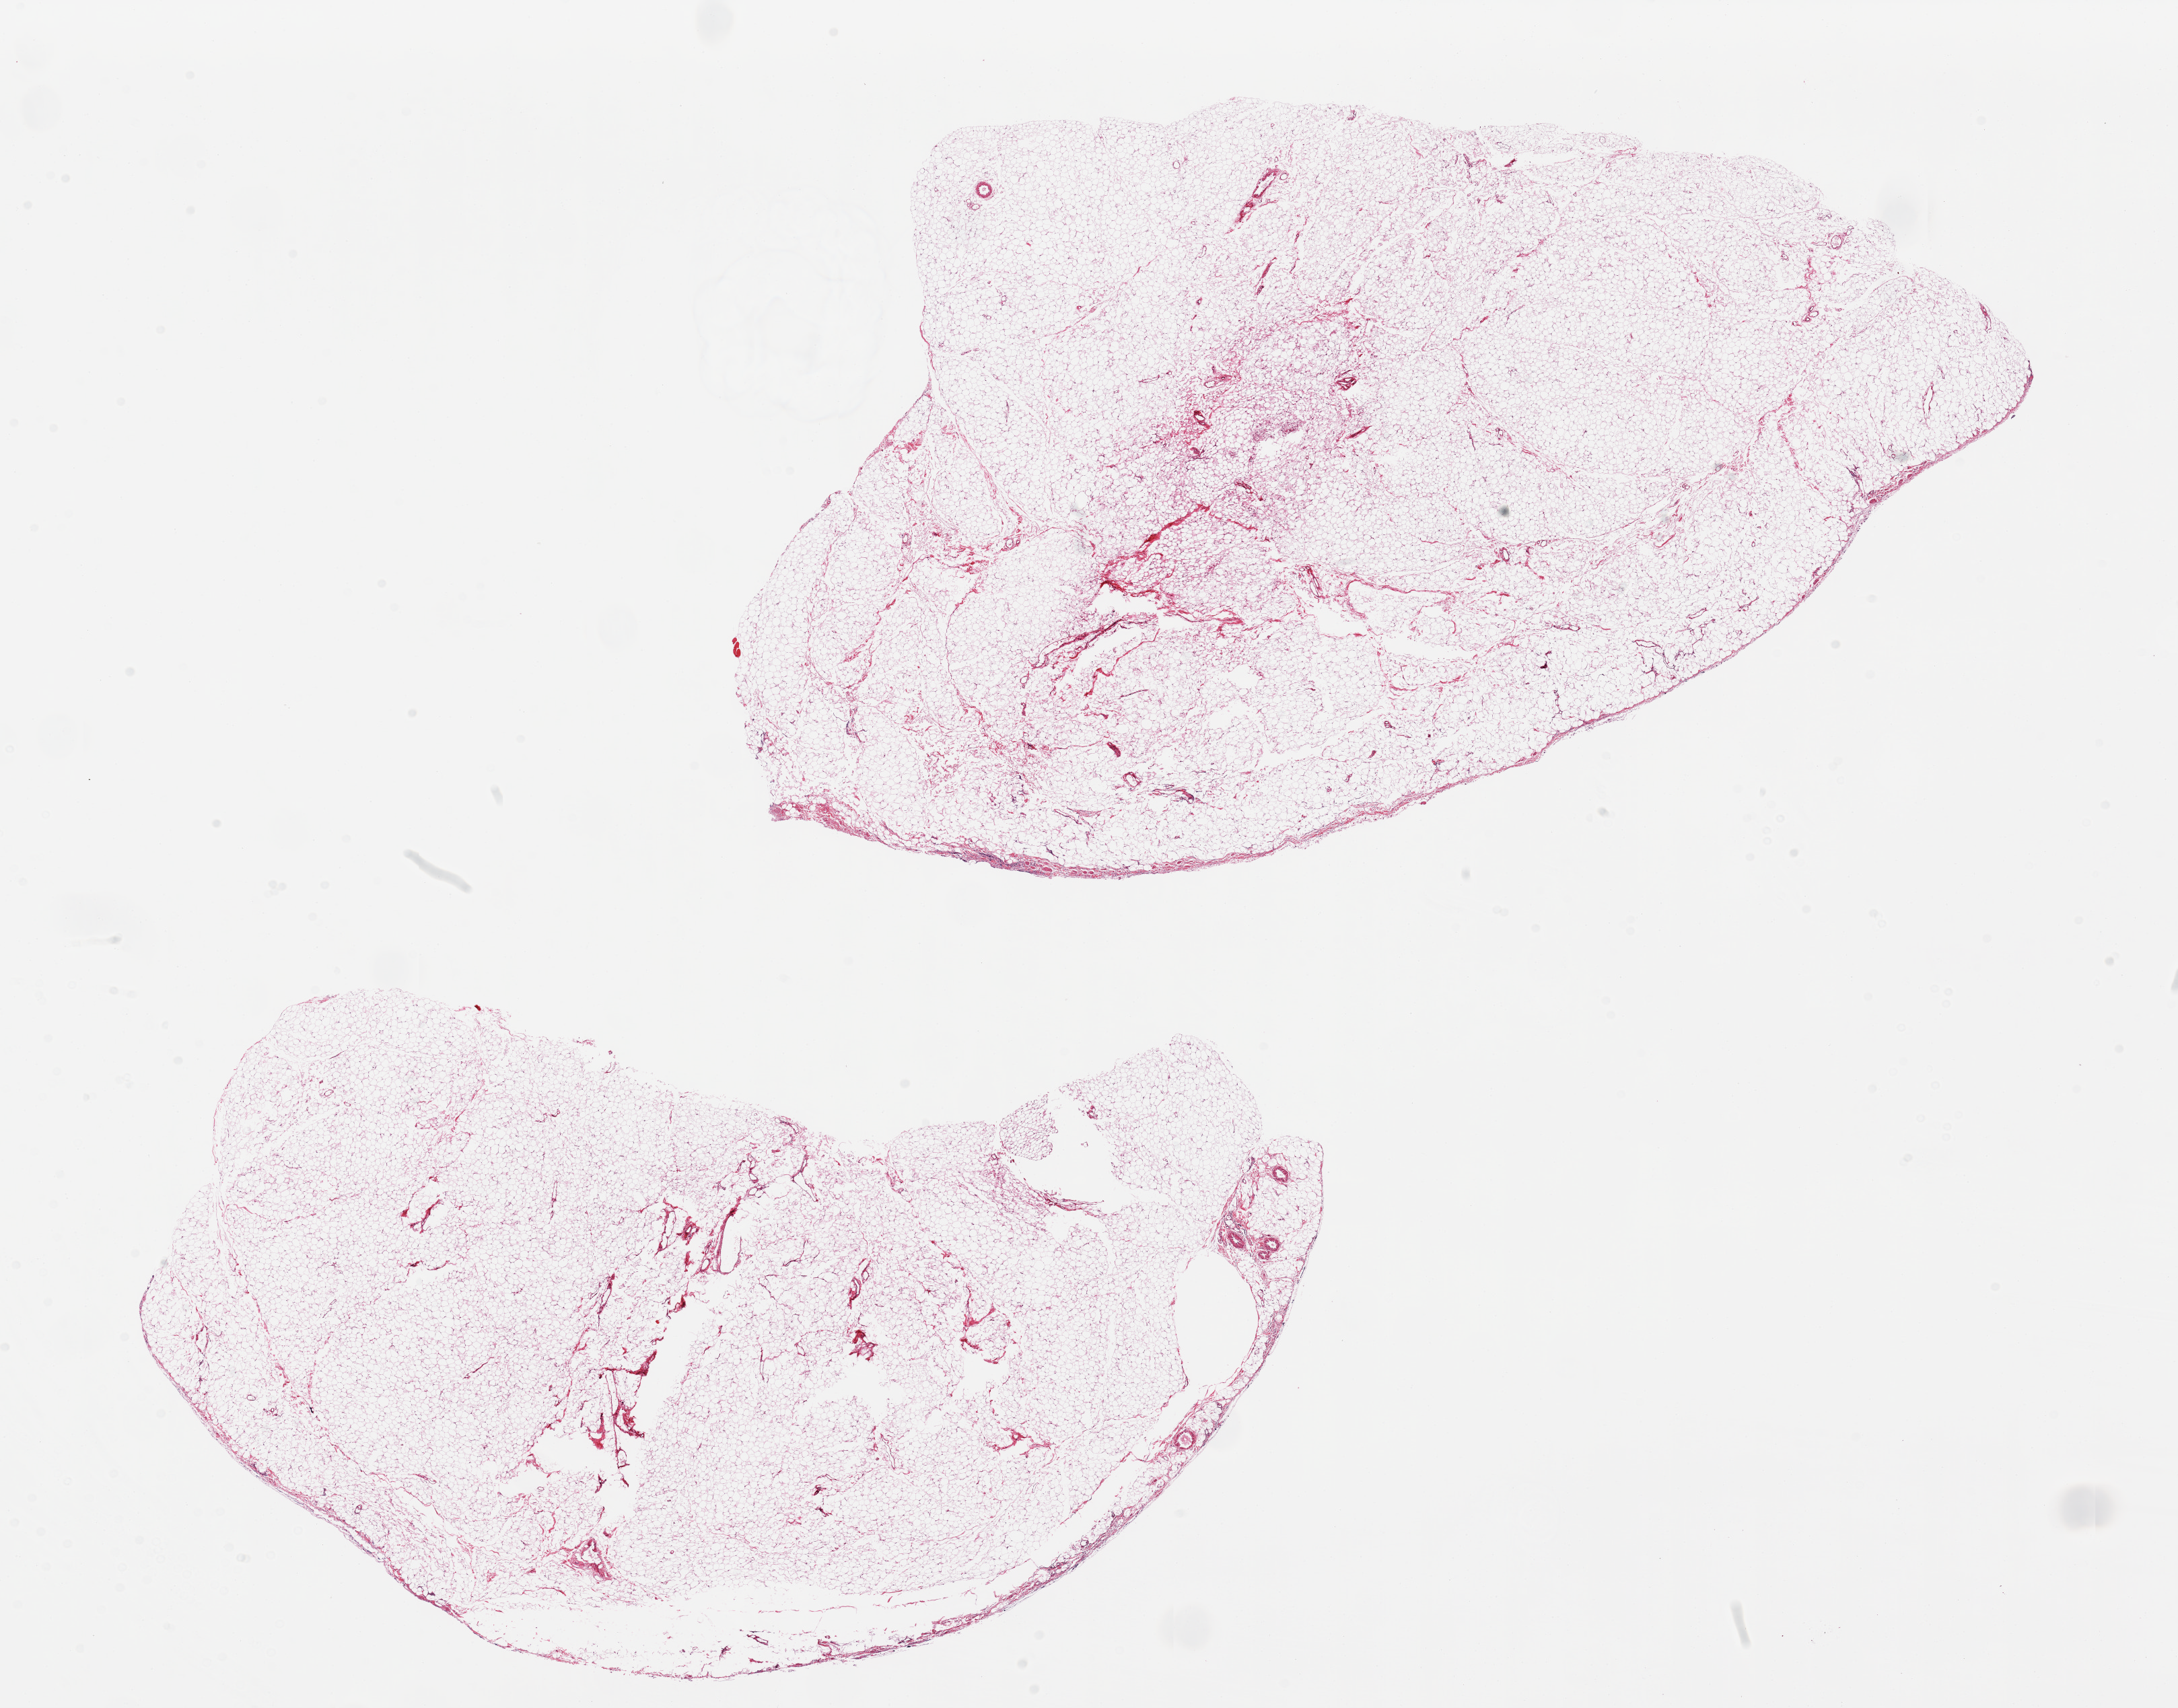
H&E whole-slide image, low-resolution overview of the scanned area, about 25.6 x 20.1 mm (acquisition: 20x scan), PAXgene-fixed paraffin-embedded (PFPE) section, sampled site (target tissue): omentum, tissue donor sample. Donor sex: female.
Review note (as recorded): 2 pieces, minimal vascularity/fibrosis.